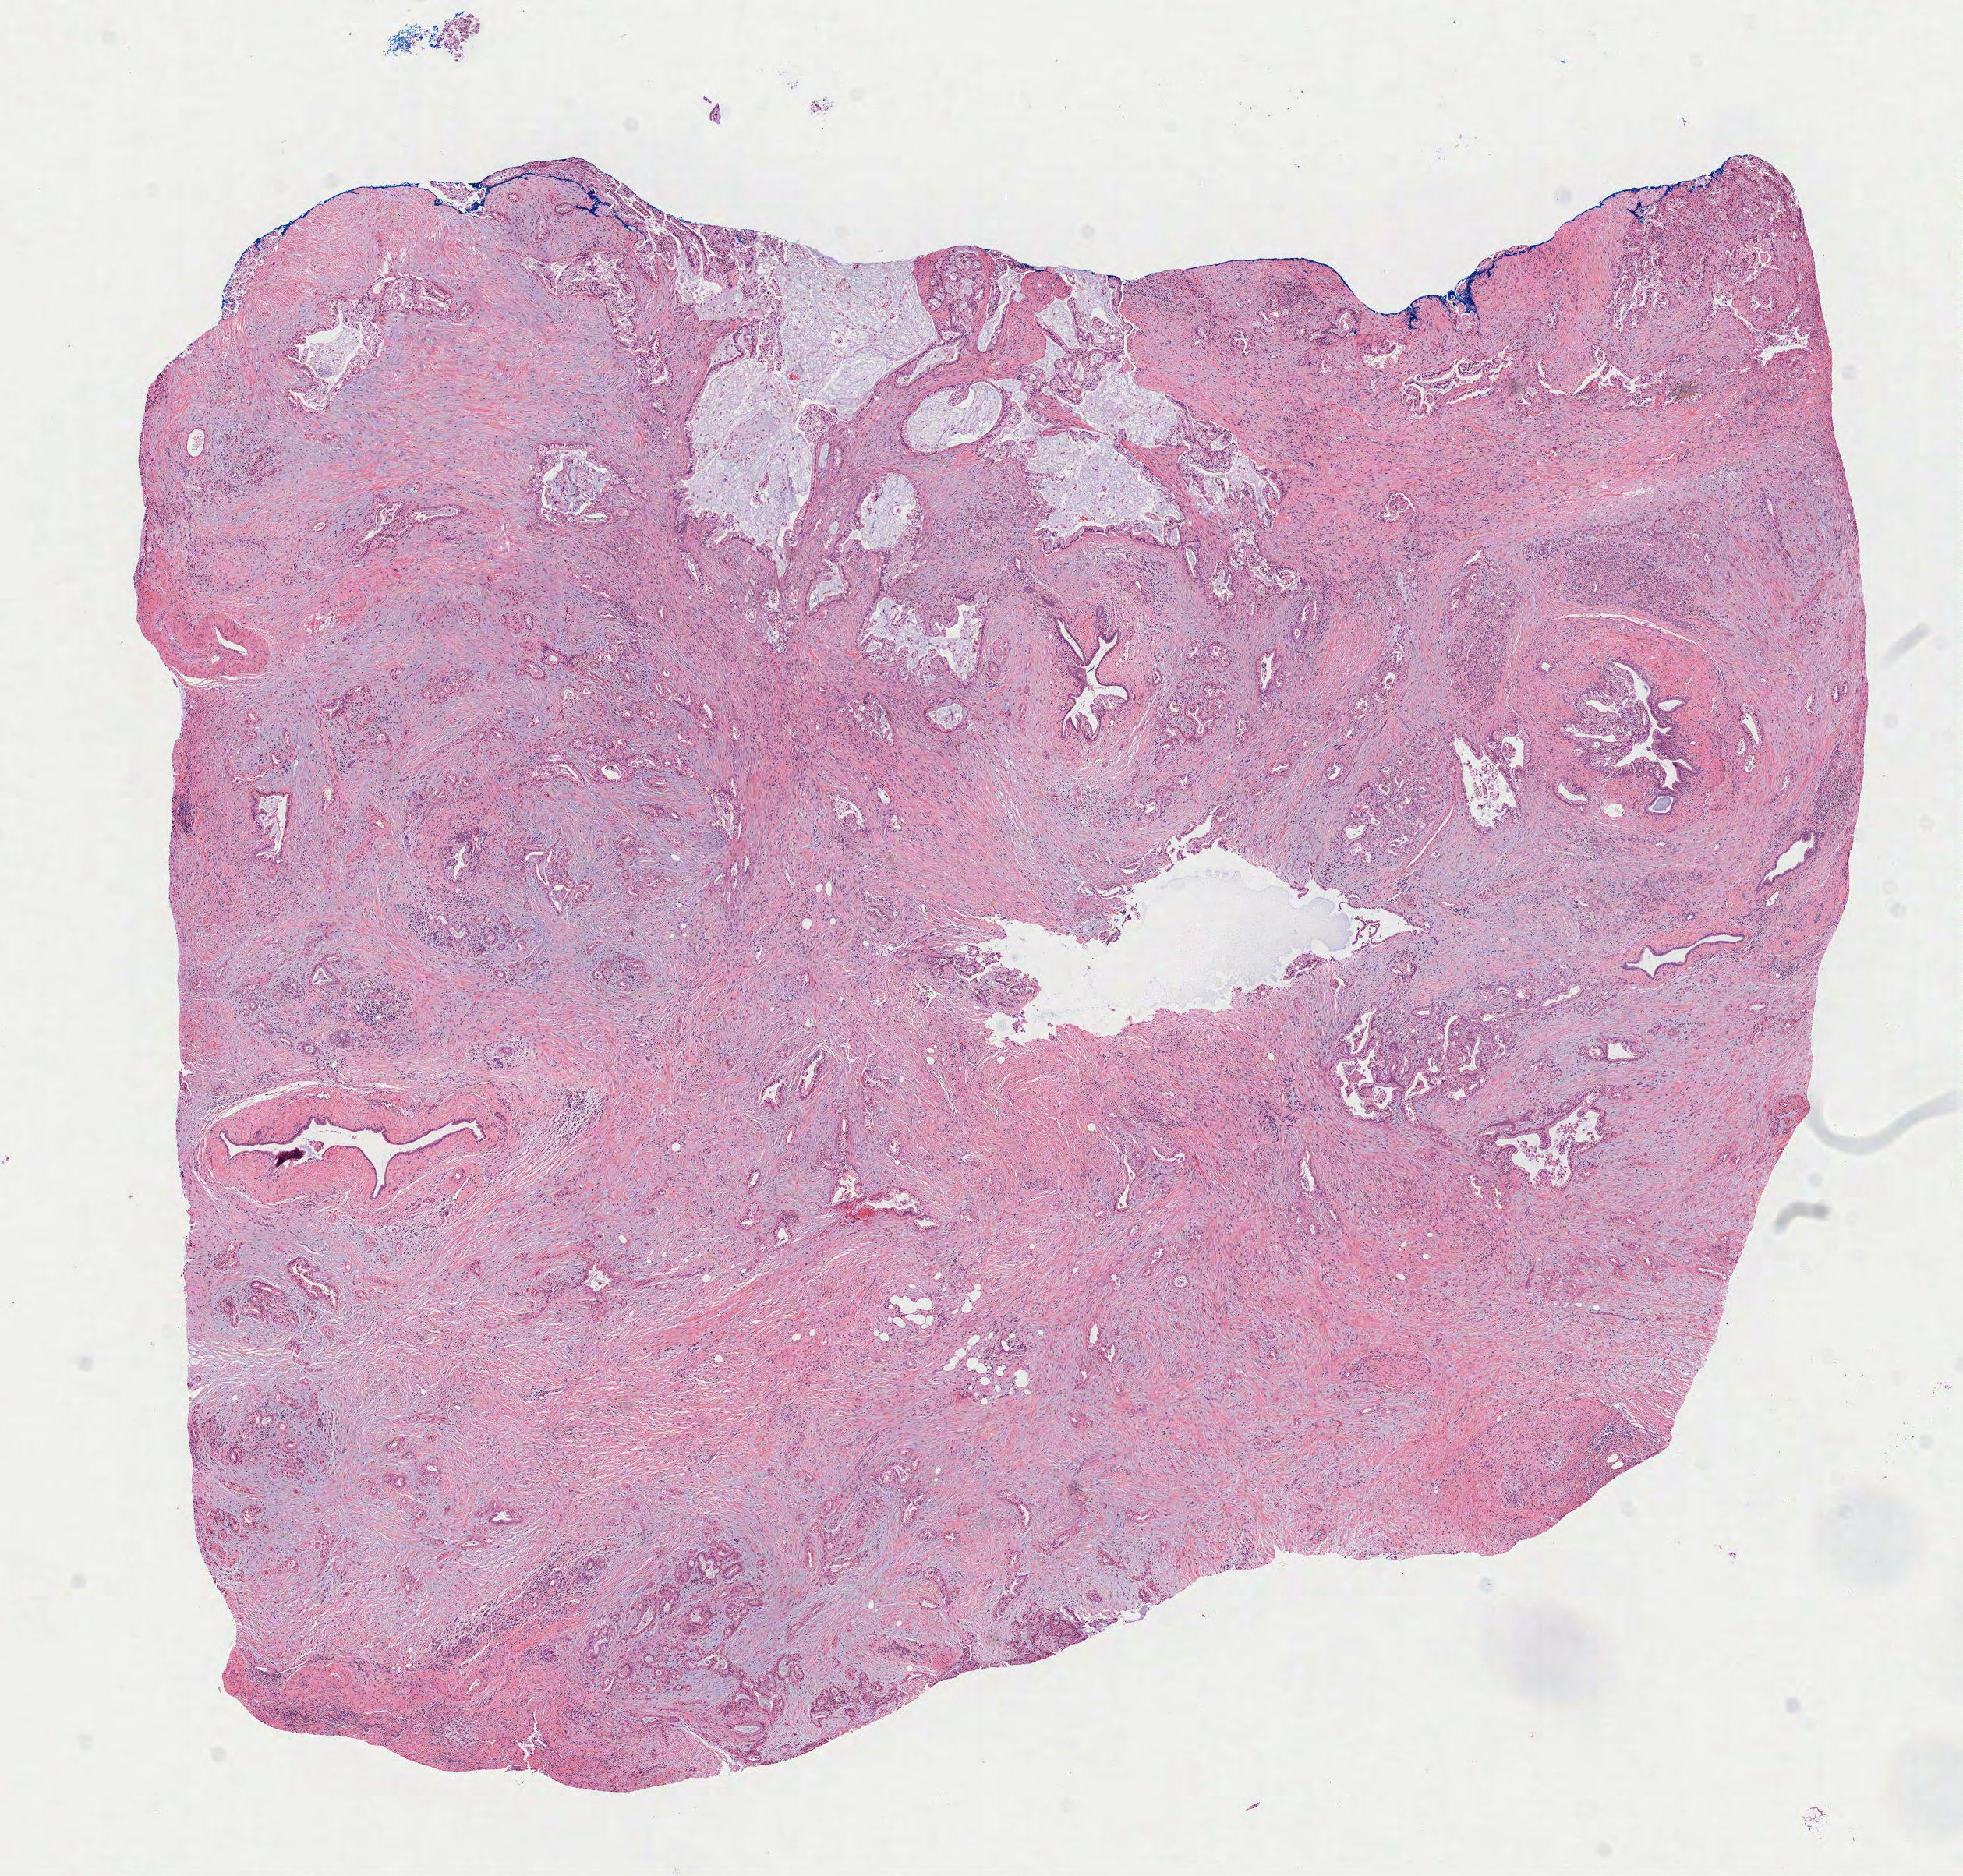
Whole-slide histology image, H&E-stained, low-resolution overview of the scanned area, about 10.2 x 9.7 mm (from a 40x scan); FFPE section; primary tumour sample from the pancreas. Patient: female, age at initial diagnosis 54 years.
Histologic diagnosis: Infiltrating duct carcinoma, NOS (head of pancreas).